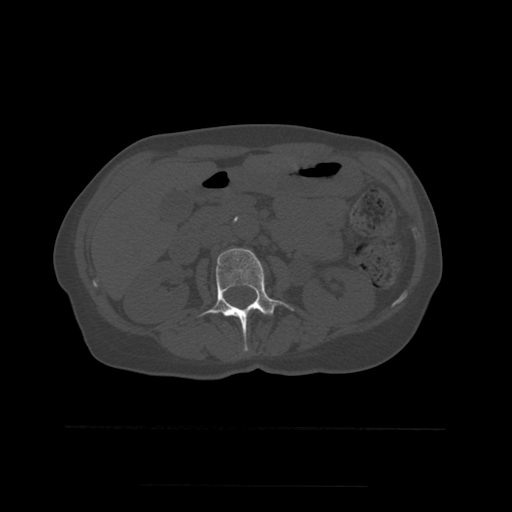
CT including the spine, one axial slice; bone window (W 1800 / L 400 HU); 512 × 512 image matrix, field of view 350 × 350 mm. Patient age 58 years. Case-level facts recorded for this patient, not image findings: primary cancer: lung.
Outlined on this slice (semi-automatic segmentation, software-assisted and operator-edited):
- L2 vertebra: bounding box (x1, y1, x2, y2) in pixels: (199, 248, 294, 351)